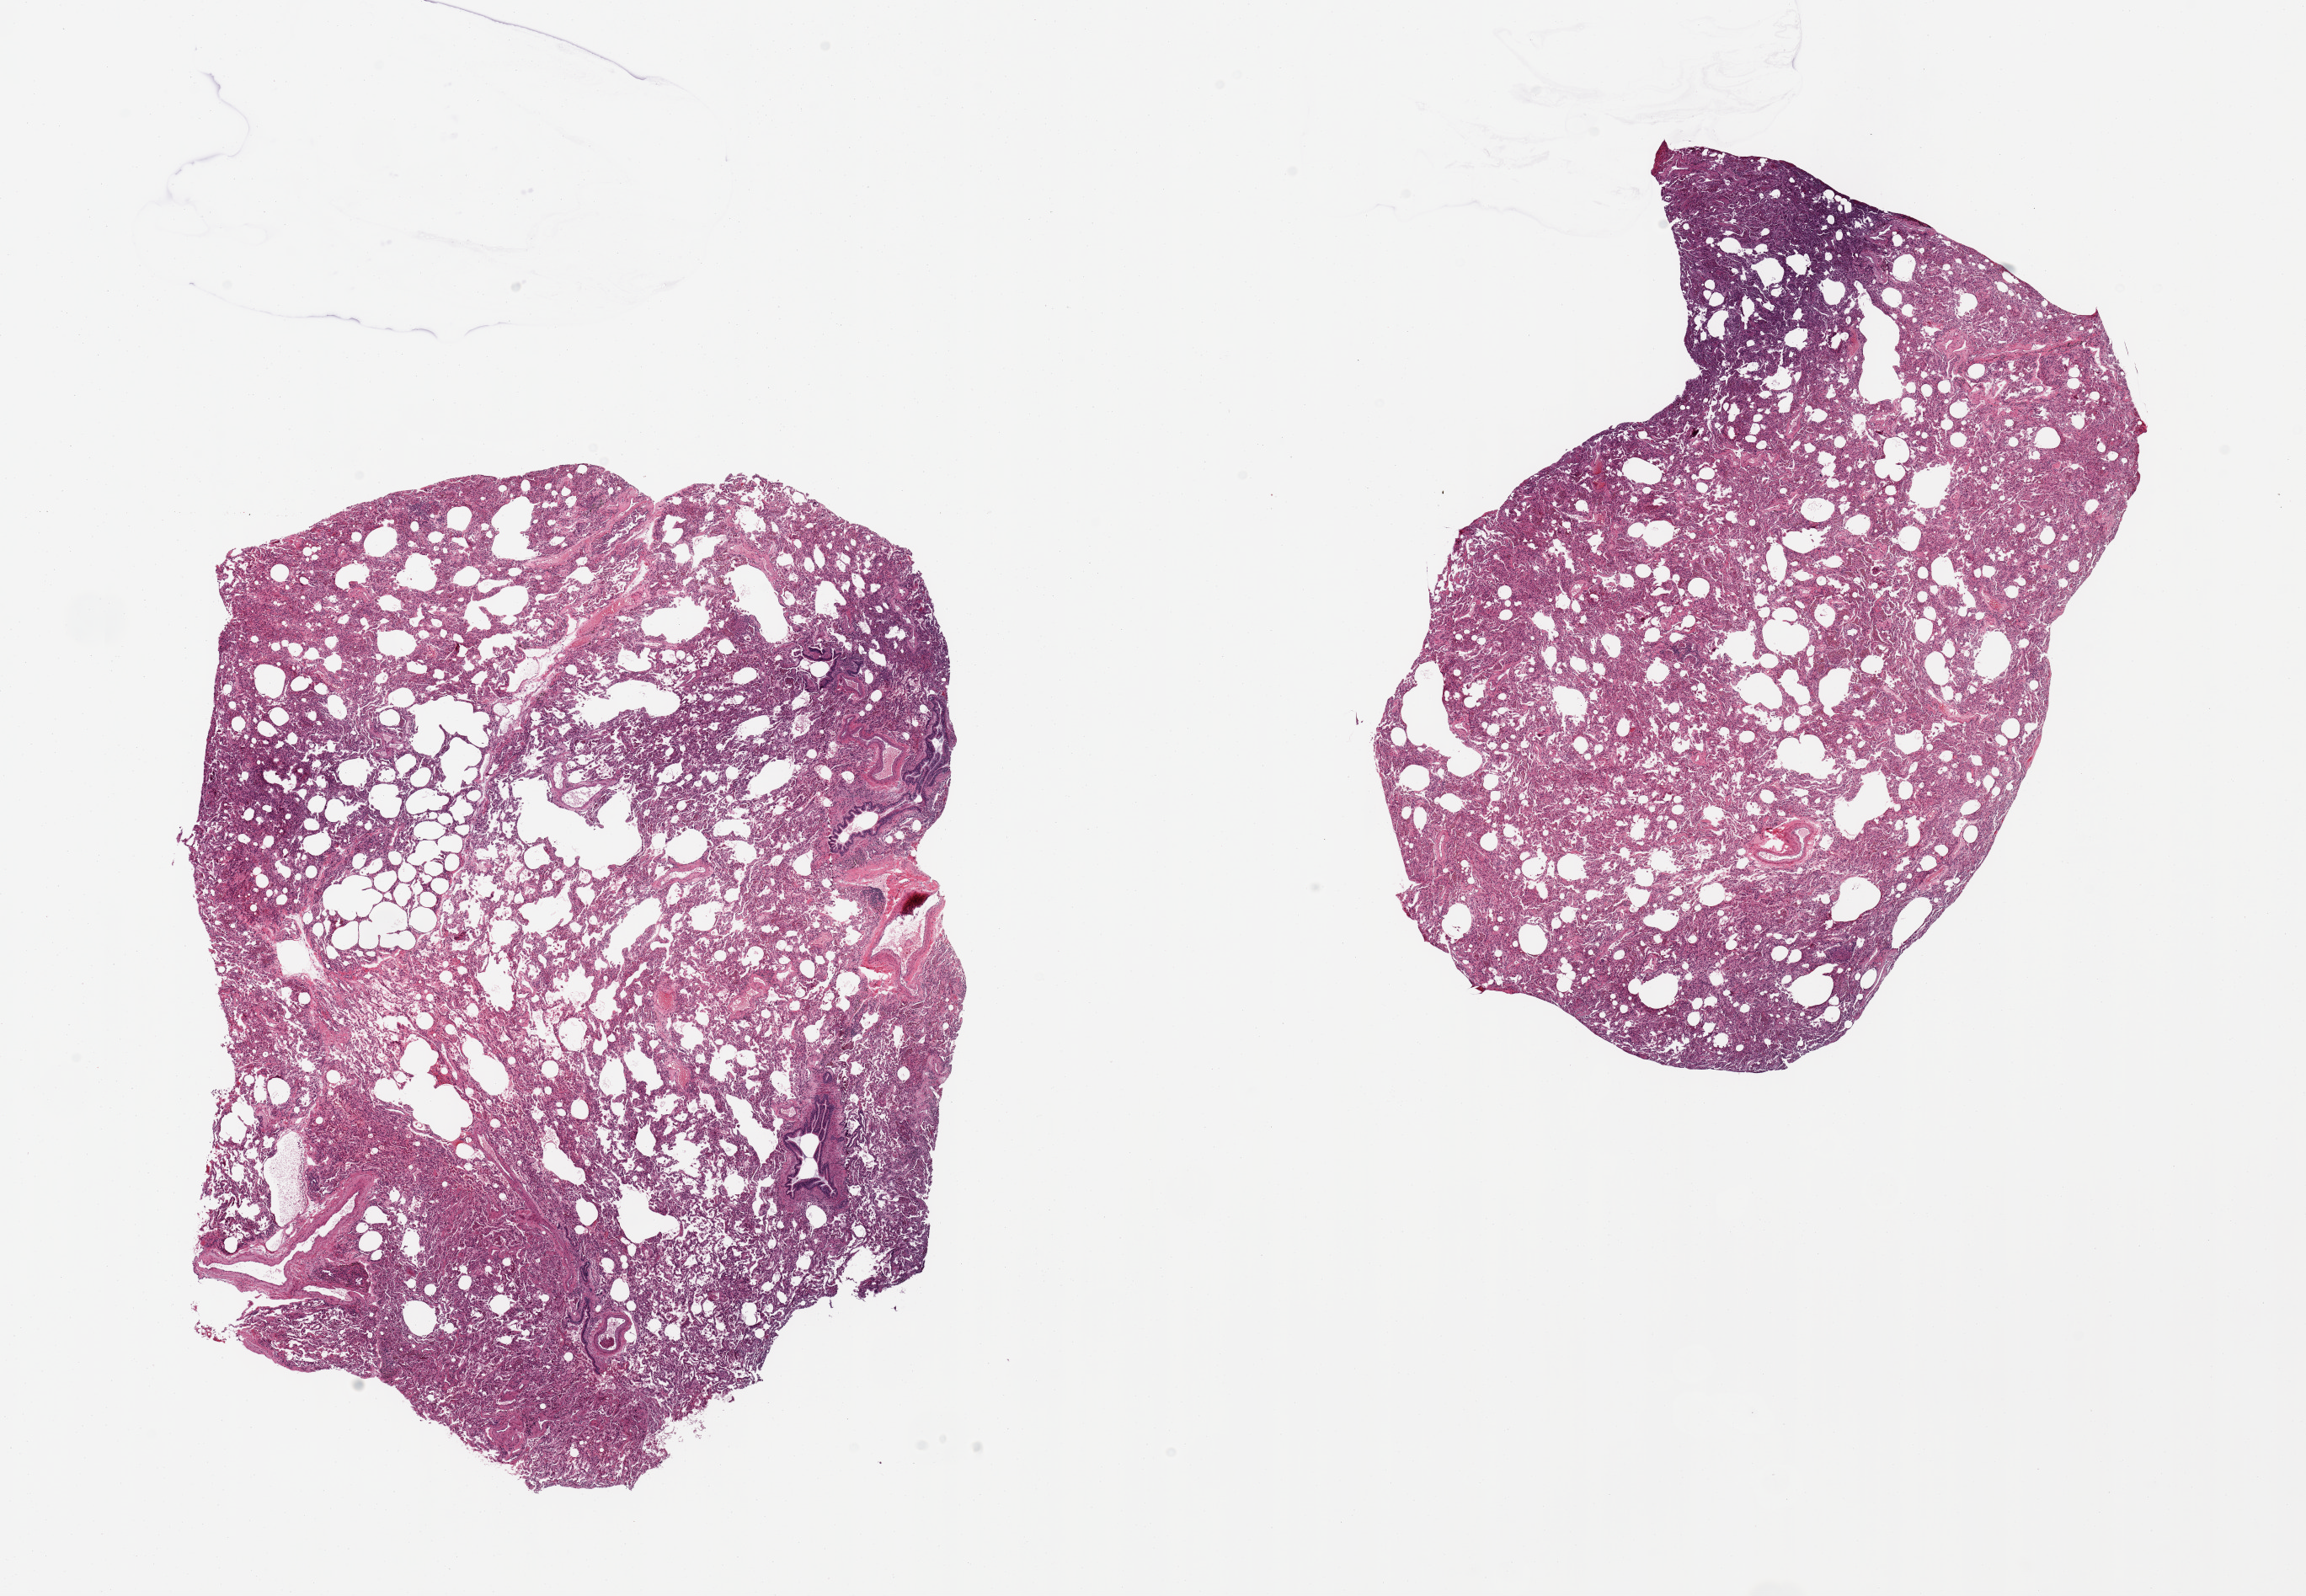
Digitized haematoxylin and eosin-stained section, brightfield — a low-resolution overview of the entire scanned area, about 21.7 x 15.0 mm (acquisition: 20x scan). PAXgene-fixed paraffin-embedded (PFPE) section. Section of lung (target tissue). Donor tissue sample. Male donor.
Pathologist's review note for this sample: 2 pieces; some collapse, numerous pulmonary macrophages.